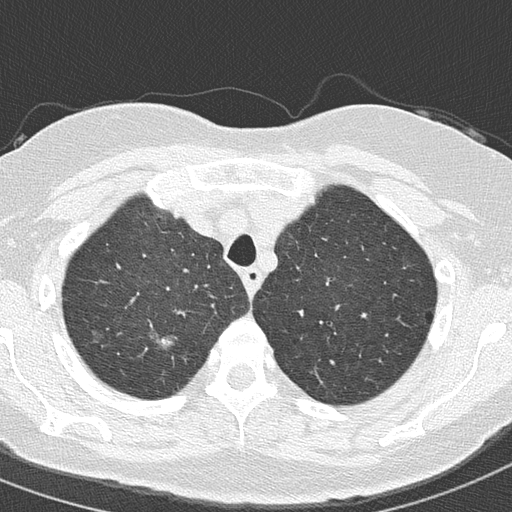
Low-dose screening chest CT, axial slice, second screening round (one year after baseline), lung window (W 1500 / L -600 HU), 2 mm slice thickness. Female, age 61 years at enrolment.
Expert reader's lesion annotation, box from (x=143, y=319) to (x=187, y=361) px. Reader record for this screening exam (exam-level; its link to the box is not recorded): non-calcified nodule or mass ≥4 mm, right upper lobe, 15 × 10 mm, spiculated (stellate) margins, ground glass attenuation, pre-existing on the prior screen: yes; interval growth: yes. Participant outcome: lung cancer diagnosed 91 days after this screen — adenocarcinoma, NOS, right upper lobe, moderately differentiated (G2), stage IA (AJCC 6th edition), 20 mm at pathology.